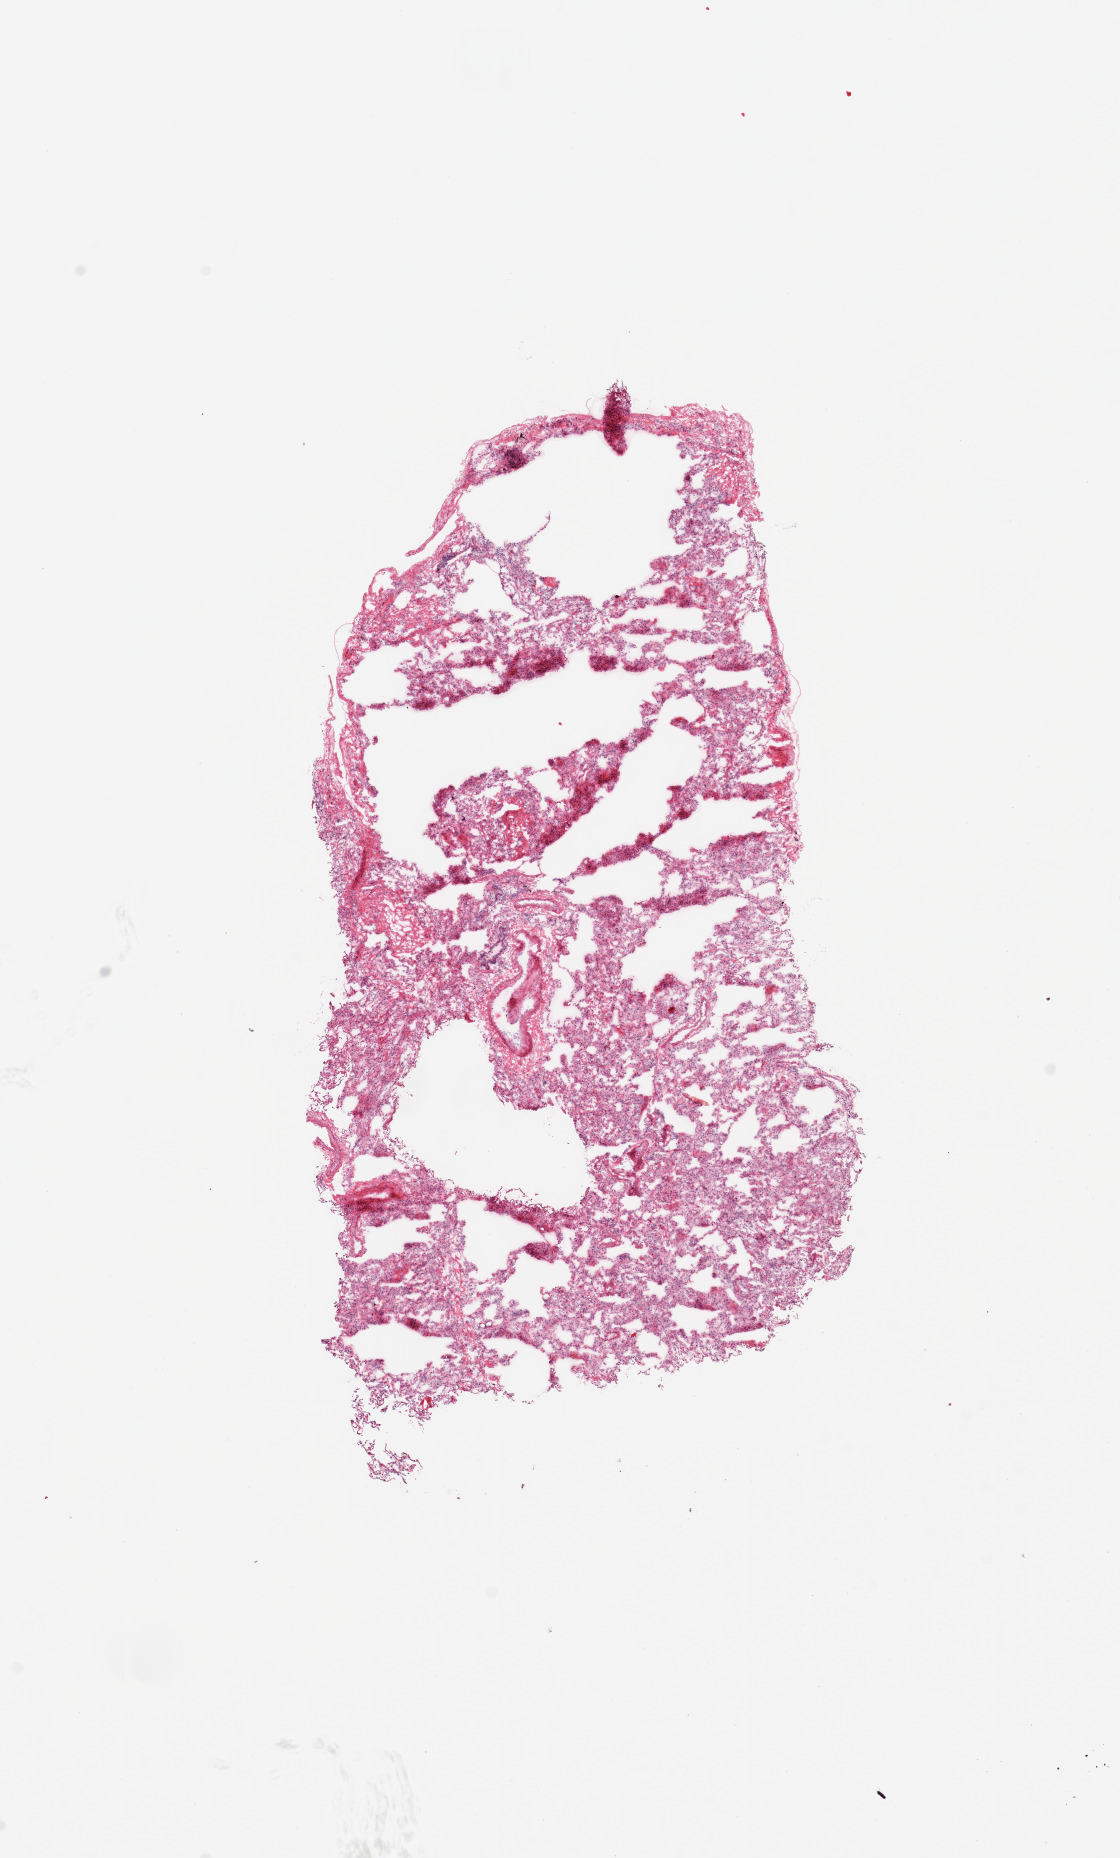
Haematoxylin and eosin whole-slide image, brightfield, a low-resolution overview of the entire scanned area, about 8.9 x 14.7 mm. Donor sex: female.
* specimen: frozen section (dry ice); section of lung (target tissue); donor tissue sample